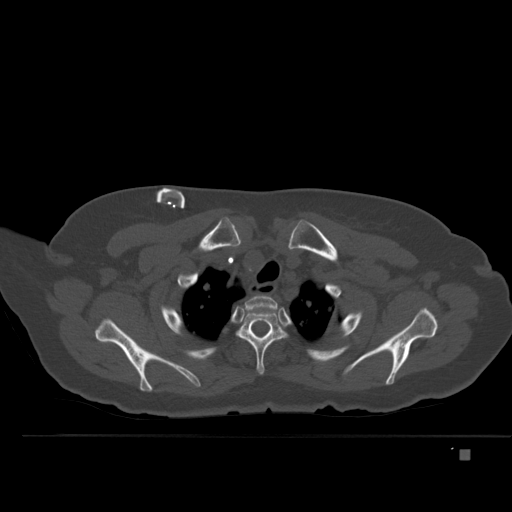
CT including the spine, one axial slice; position 392 of 477 along the scan axis; bone window (W 1800 / L 400 HU); 1.5 mm slice thickness; 512 × 512 image matrix. Patient: female, 74 years. From the clinical record (not read from this slice): primary cancer: colon.
Outlined on this slice (semi-automatically segmented with operator editing):
- T1 vertebra: box from (x=232, y=296) to (x=277, y=323) px
- T2 vertebra: (x=237, y=307)–(x=291, y=375)